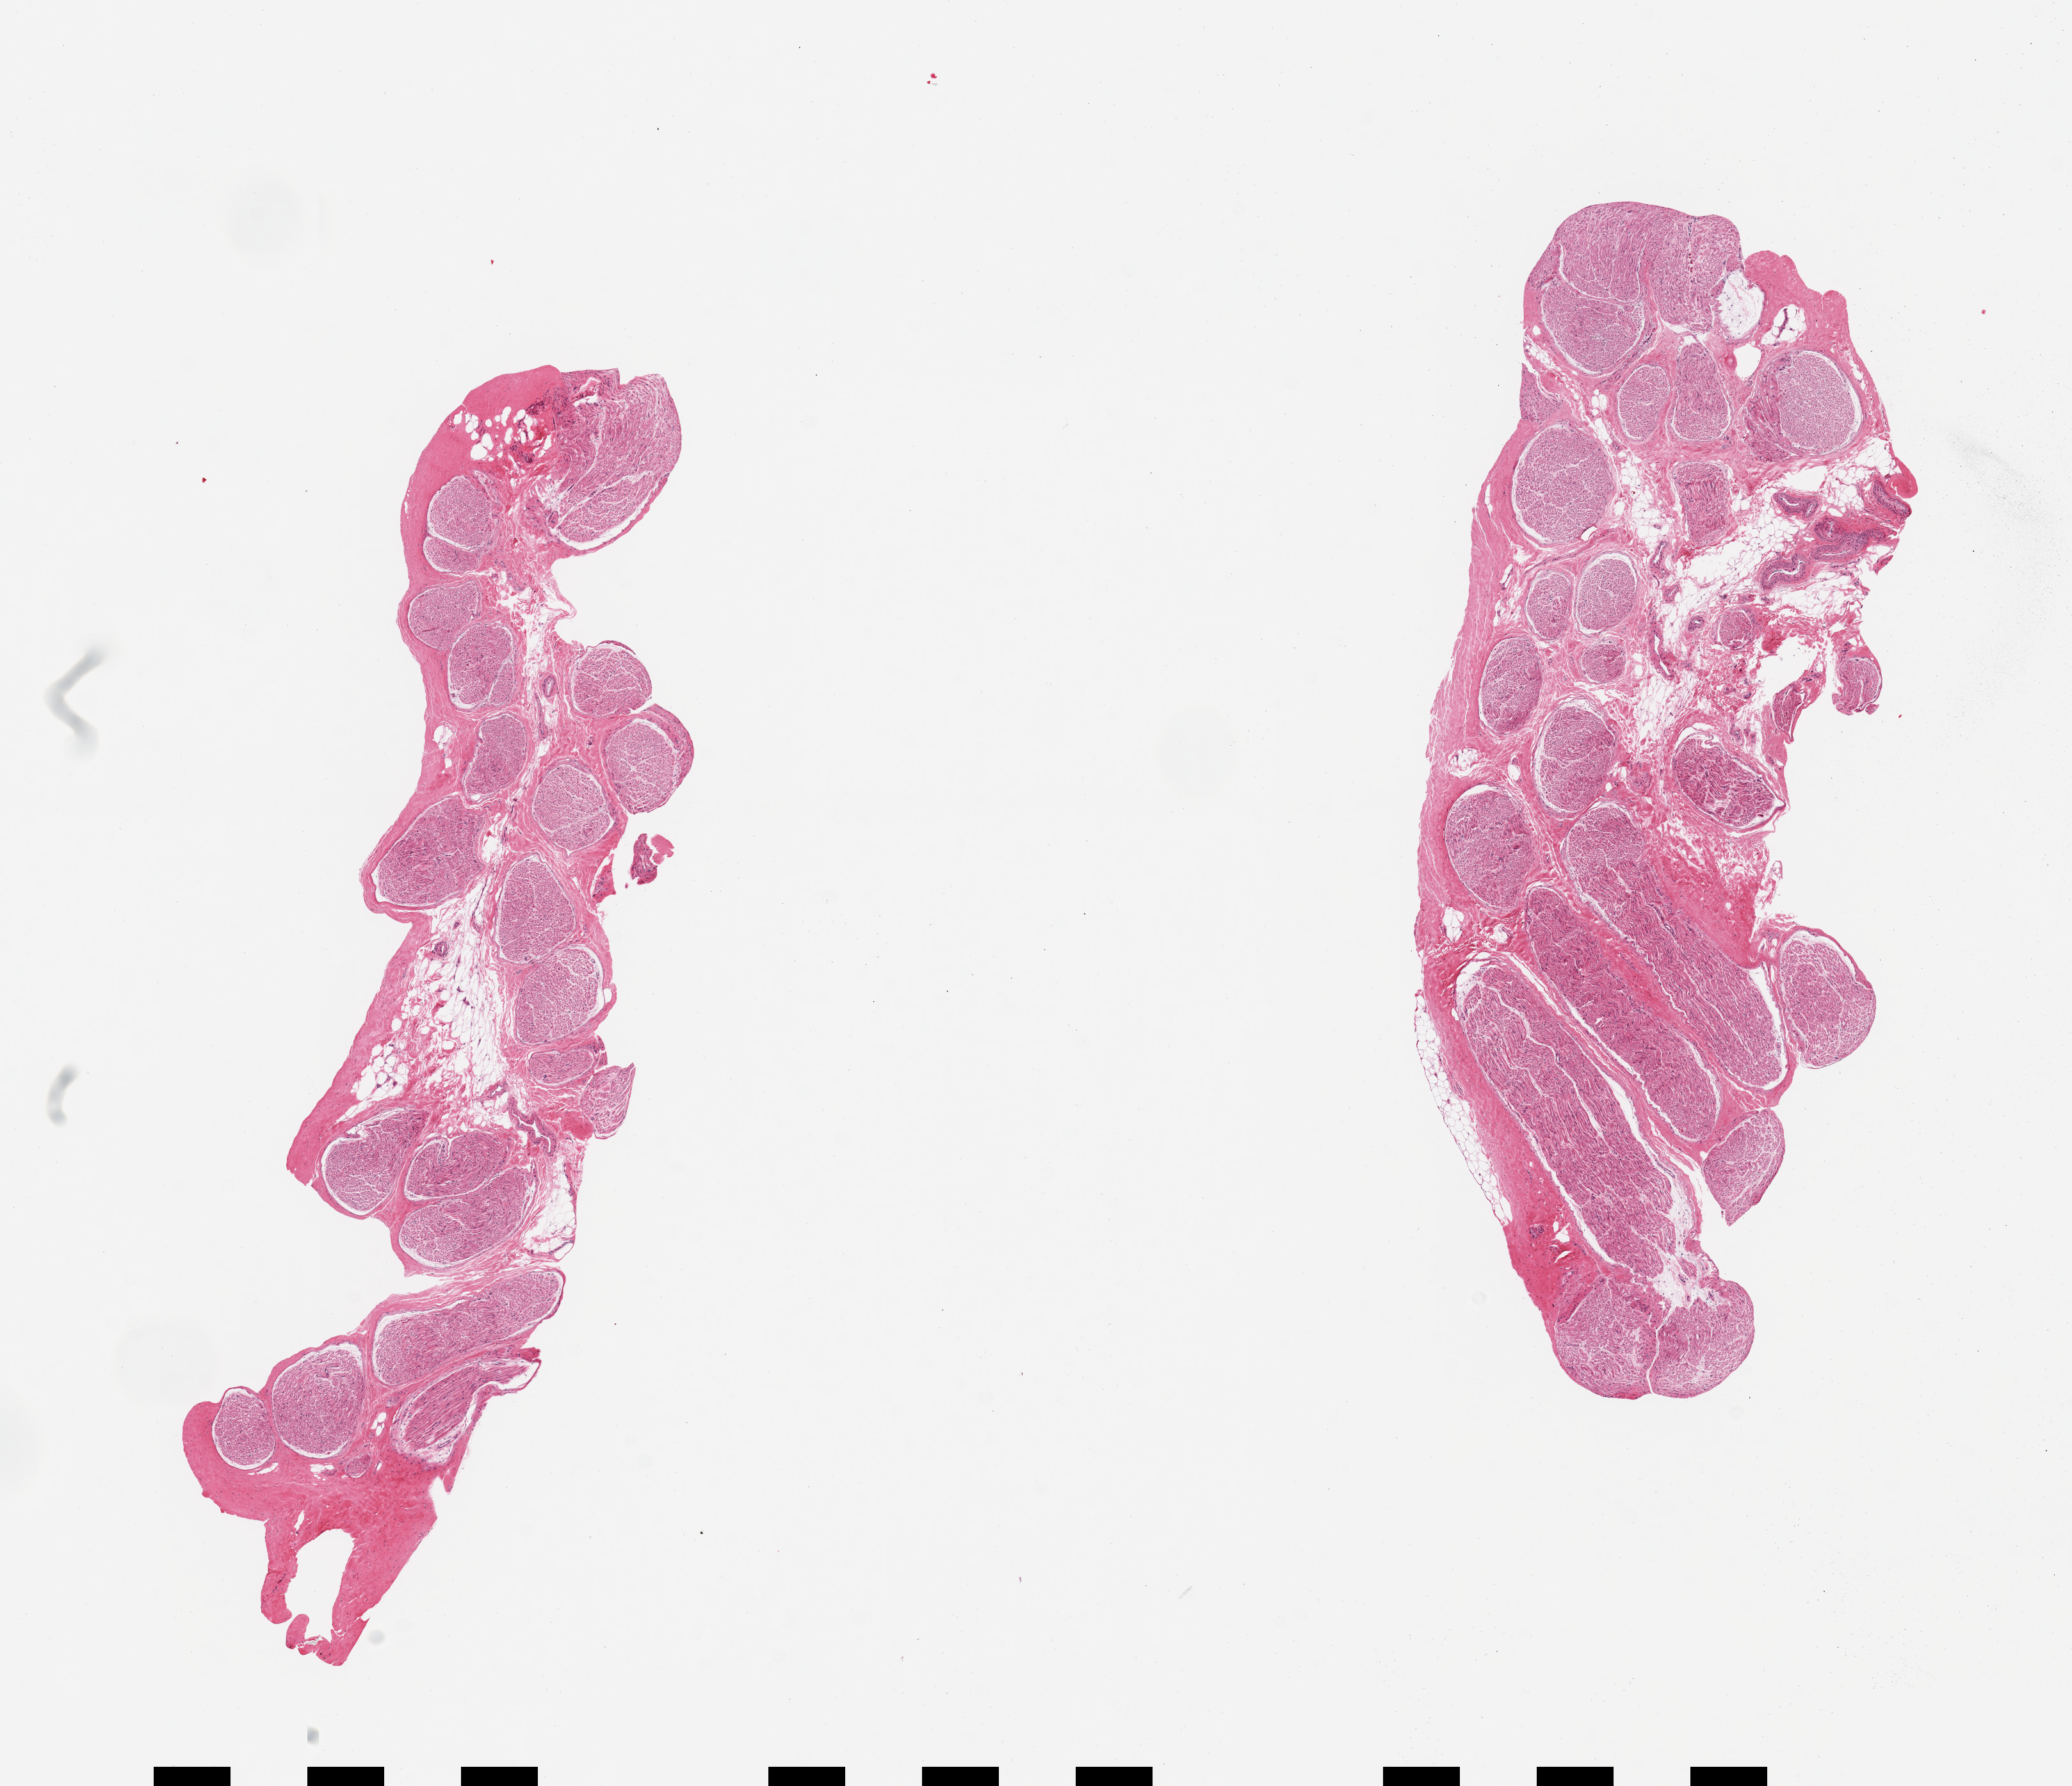
Haematoxylin and eosin whole-slide image, brightfield, whole scanned area (about 12.8 x 11.0 mm, acquisition: 20x scan) shown as a low-resolution overview. PAXgene-fixed, paraffin-embedded tissue. Section of tibial nerve (target tissue). Donor tissue sample. Donor: male.
Reviewer comment on this tissue sample: 2 pieces; 10% internal fat content; well trimmed.